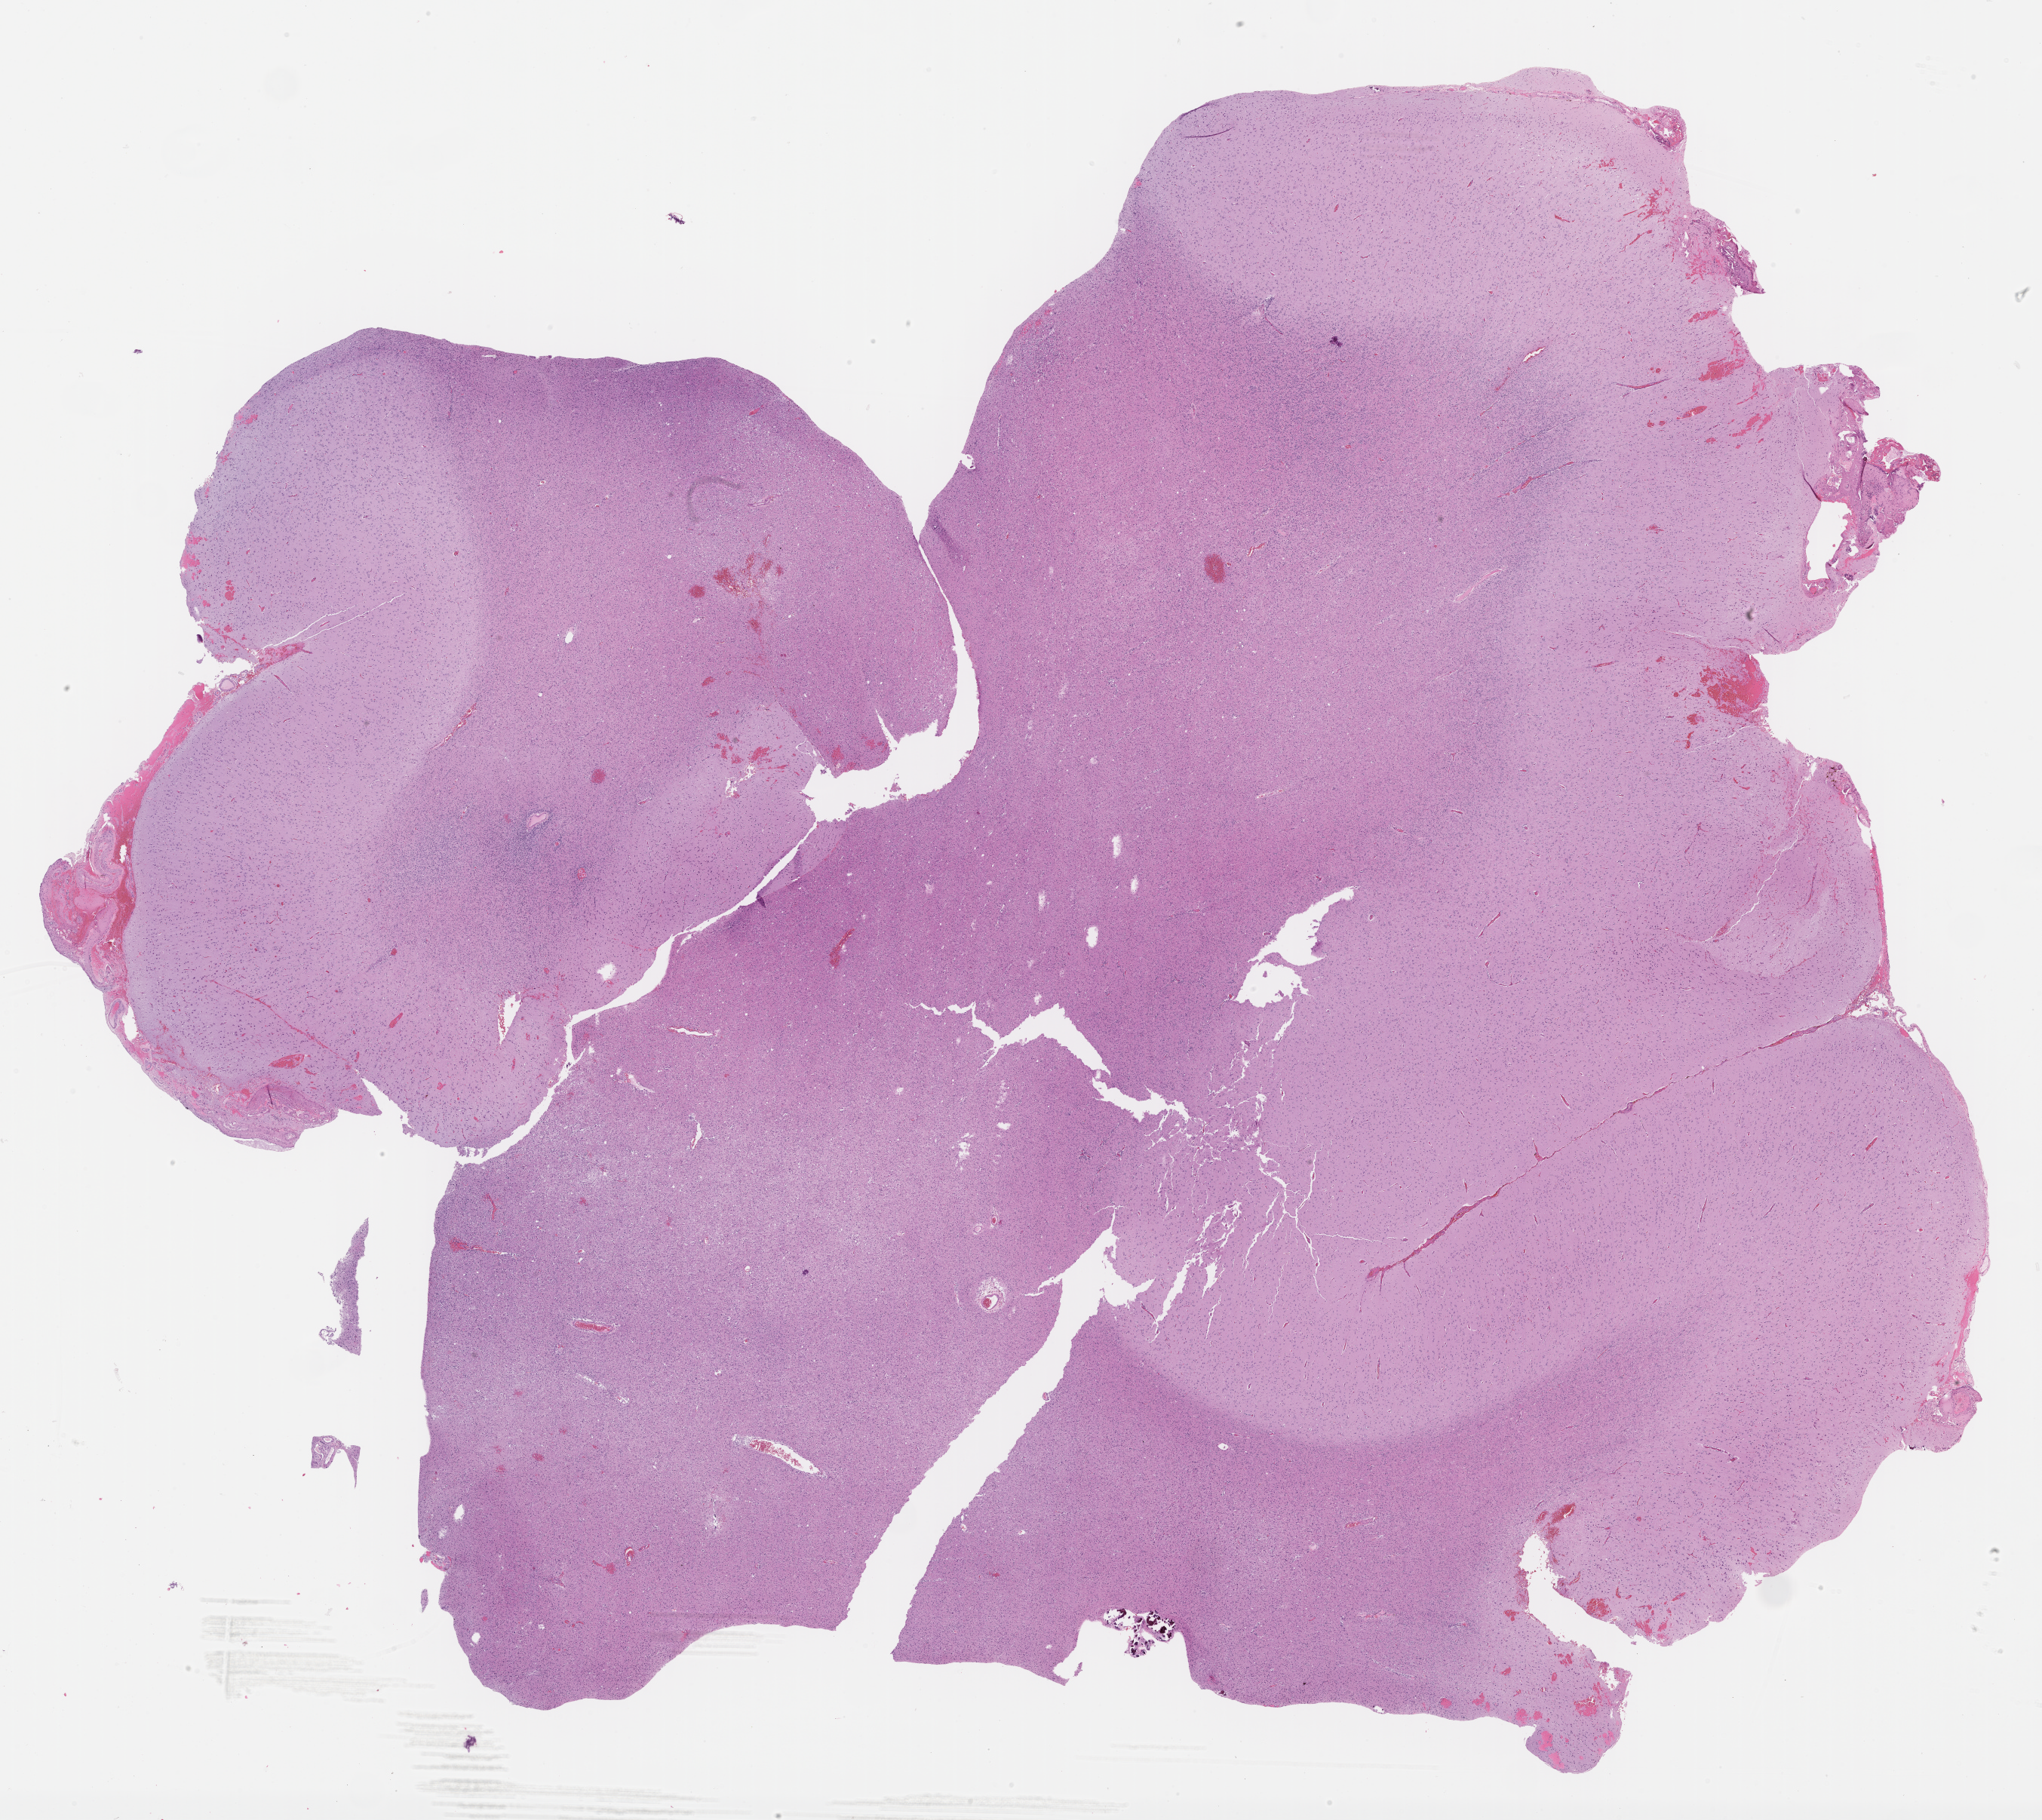
Digitized H&E-stained tissue section (whole slide) — shown as a low-resolution overview of the whole scanned area (about 21.8 x 19.4 mm). Formalin-fixed paraffin-embedded (FFPE) diagnostic section. Sample: primary tumour, brain. Patient: female, age at initial diagnosis 53 years. Histologic grade: G2 (moderately differentiated).
Diagnosis: Oligodendroglioma, NOS (cerebrum).